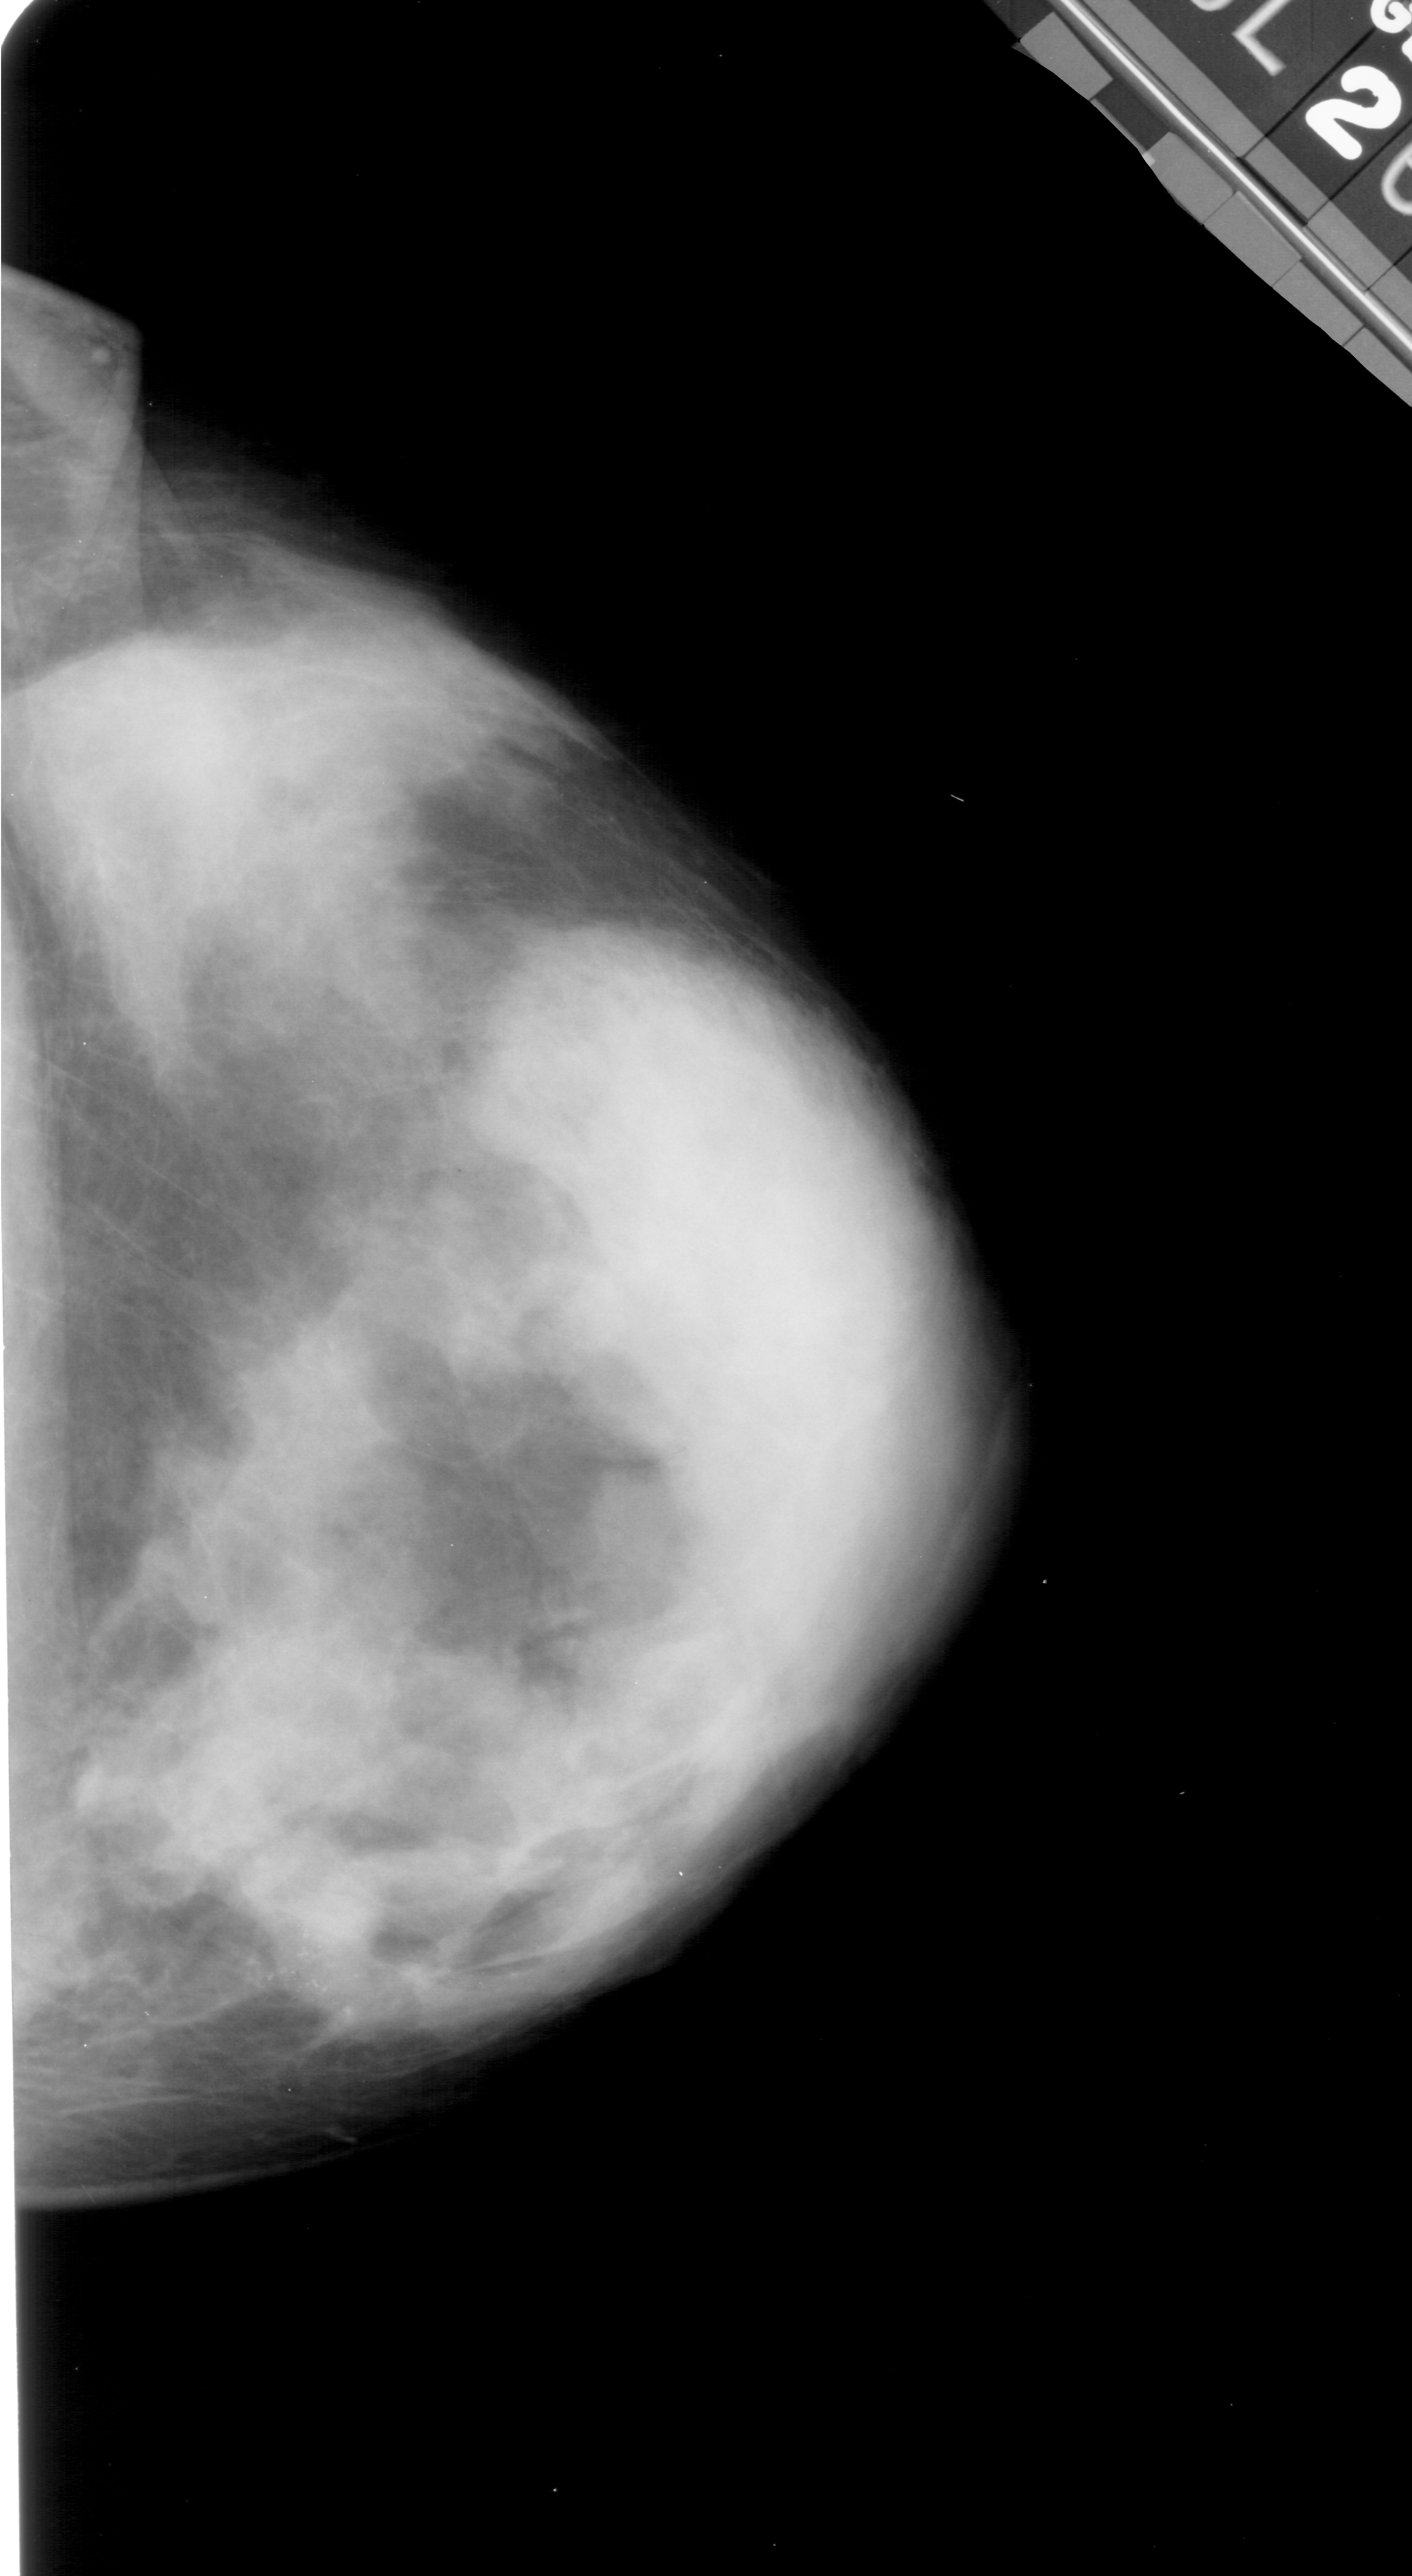
Scanned film-screen mammogram, right breast, craniocaudal (CC) view, breast composition: extremely dense (BI-RADS density category 4 of 4).
- Radiologist-marked abnormalities on this image: calcifications, morphology pleomorphic, distribution clustered; BI-RADS assessment category 4; subtlety rating 3 on a 1 (subtle) to 5 (obvious) scale; pathology result (as recorded, not read from the image): malignant.